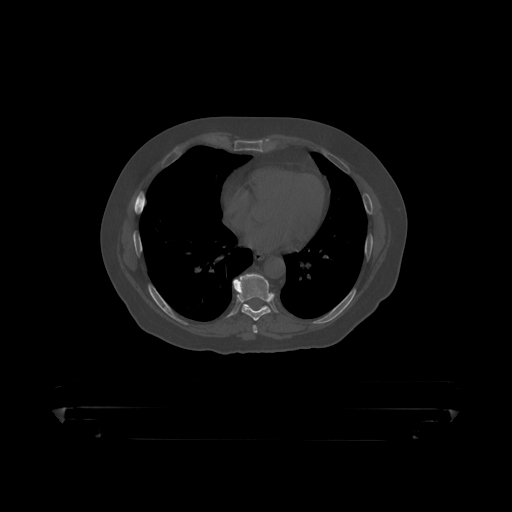
CT including the spine, one axial slice. Reconstruction kernel STANDARD. Bone window (W 1800 / L 400 HU). 1.25 mm slice thickness. 512 × 512 image matrix. Male patient, age 60 years. From the clinical record (not read from this slice): primary cancer: prostate.
Structures marked on this image (semi-automatically segmented with operator editing):
- T8 vertebra: bounding box [x1, y1, x2, y2] px = [233, 274, 273, 319]
- T9 vertebra: [237, 279, 267, 309]